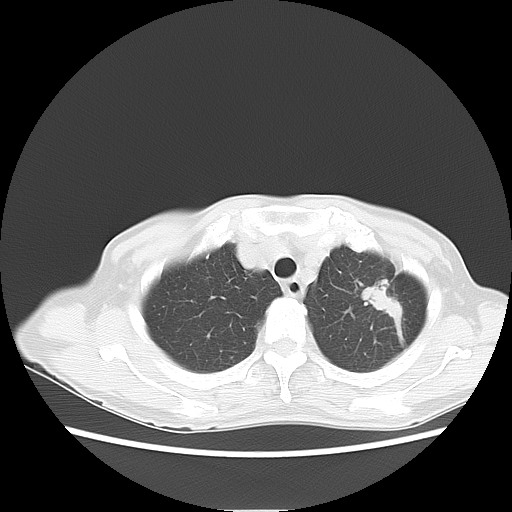
Chest CT, one axial slice. Position 10 of 13 along the scan axis. Lung window (W 1500 / L -600 HU). 512 × 512 image matrix. Patient: female, 71 years. From the clinical record (not read from this slice): clinical TNM (as recorded): T2 N0 M0.
Outlined on this slice (rectangle marked by the reading radiologist):
- lung tumour (recorded histology: adenocarcinoma): bounding box [x1, y1, x2, y2] px = [357, 280, 407, 324]